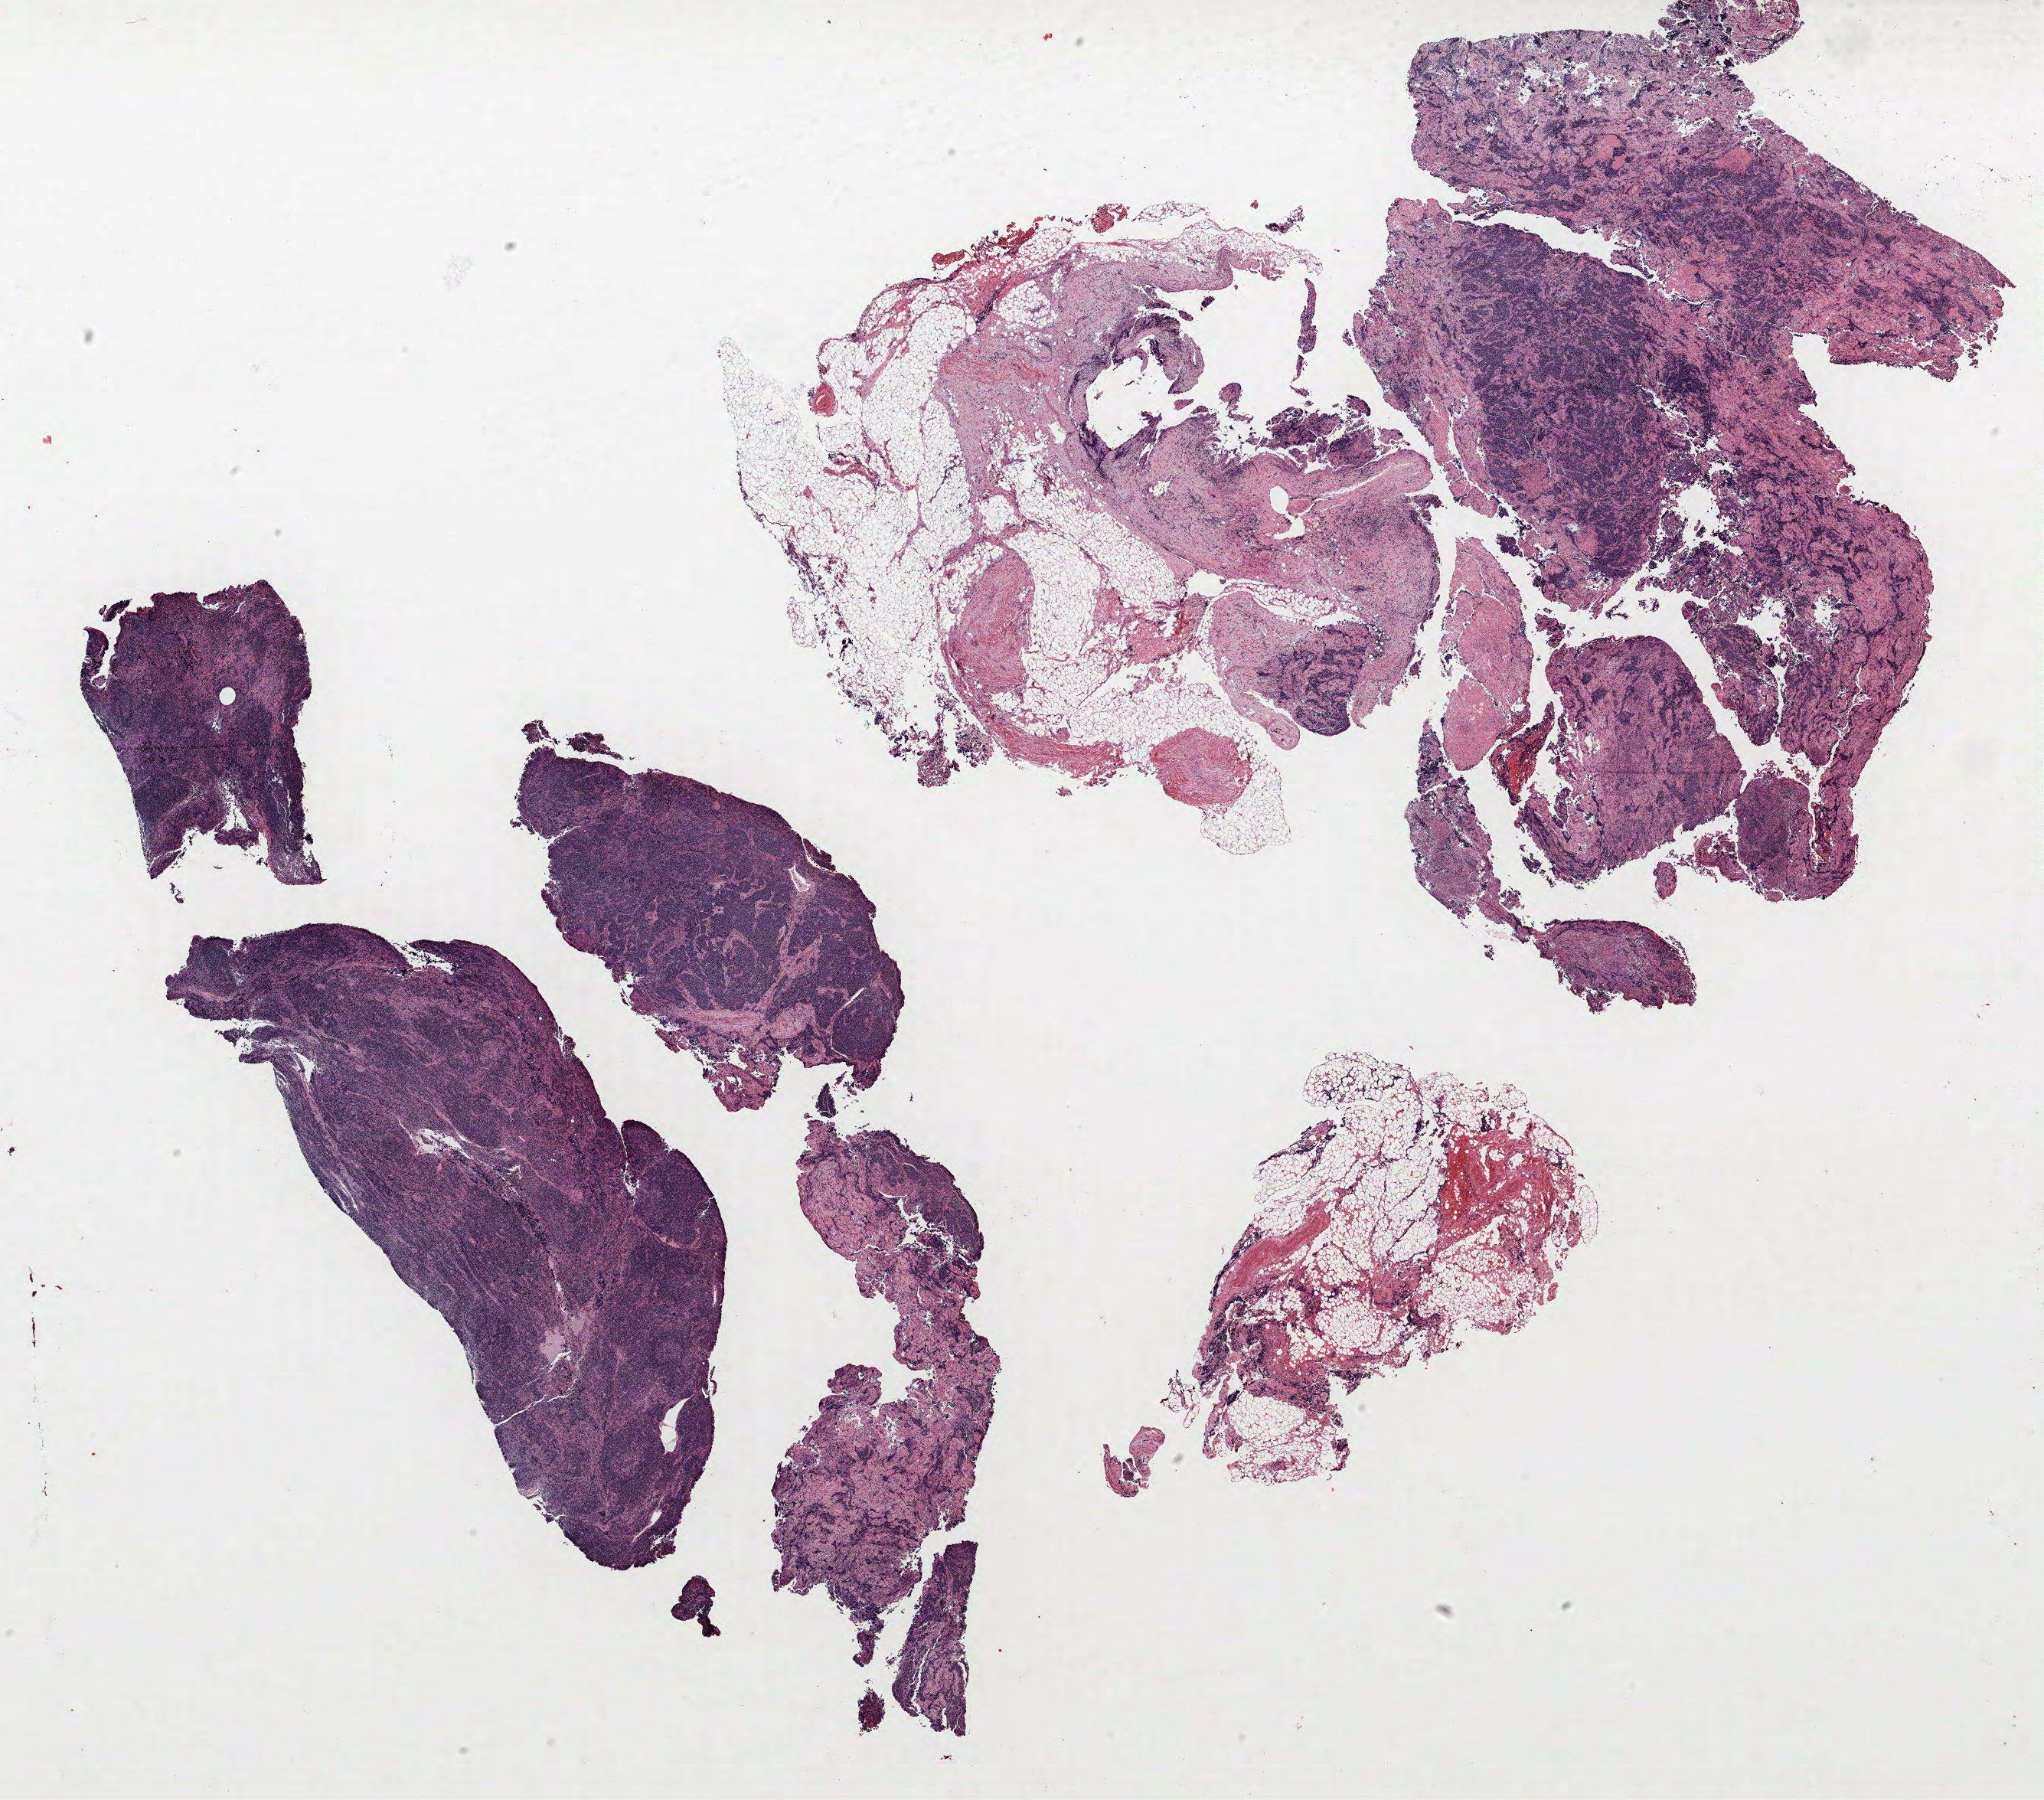
H&E-stained whole-slide image — a low-resolution overview of the entire scanned area, about 21.4 x 18.8 mm, FFPE section, lung. Female patient, aged 68 at enrolment. Current smoker at enrolment. Grade: cannot be assessed (GX).
• primary tumour location (clinical record): left upper lobe
• tumour size (pathology): 124 mm
• participant's lung-cancer diagnosis: Small cell carcinoma, NOS
• ICD-O-3 topography: upper lobe of lung (C34.1)
• stage (AJCC 6th edition): IIIA